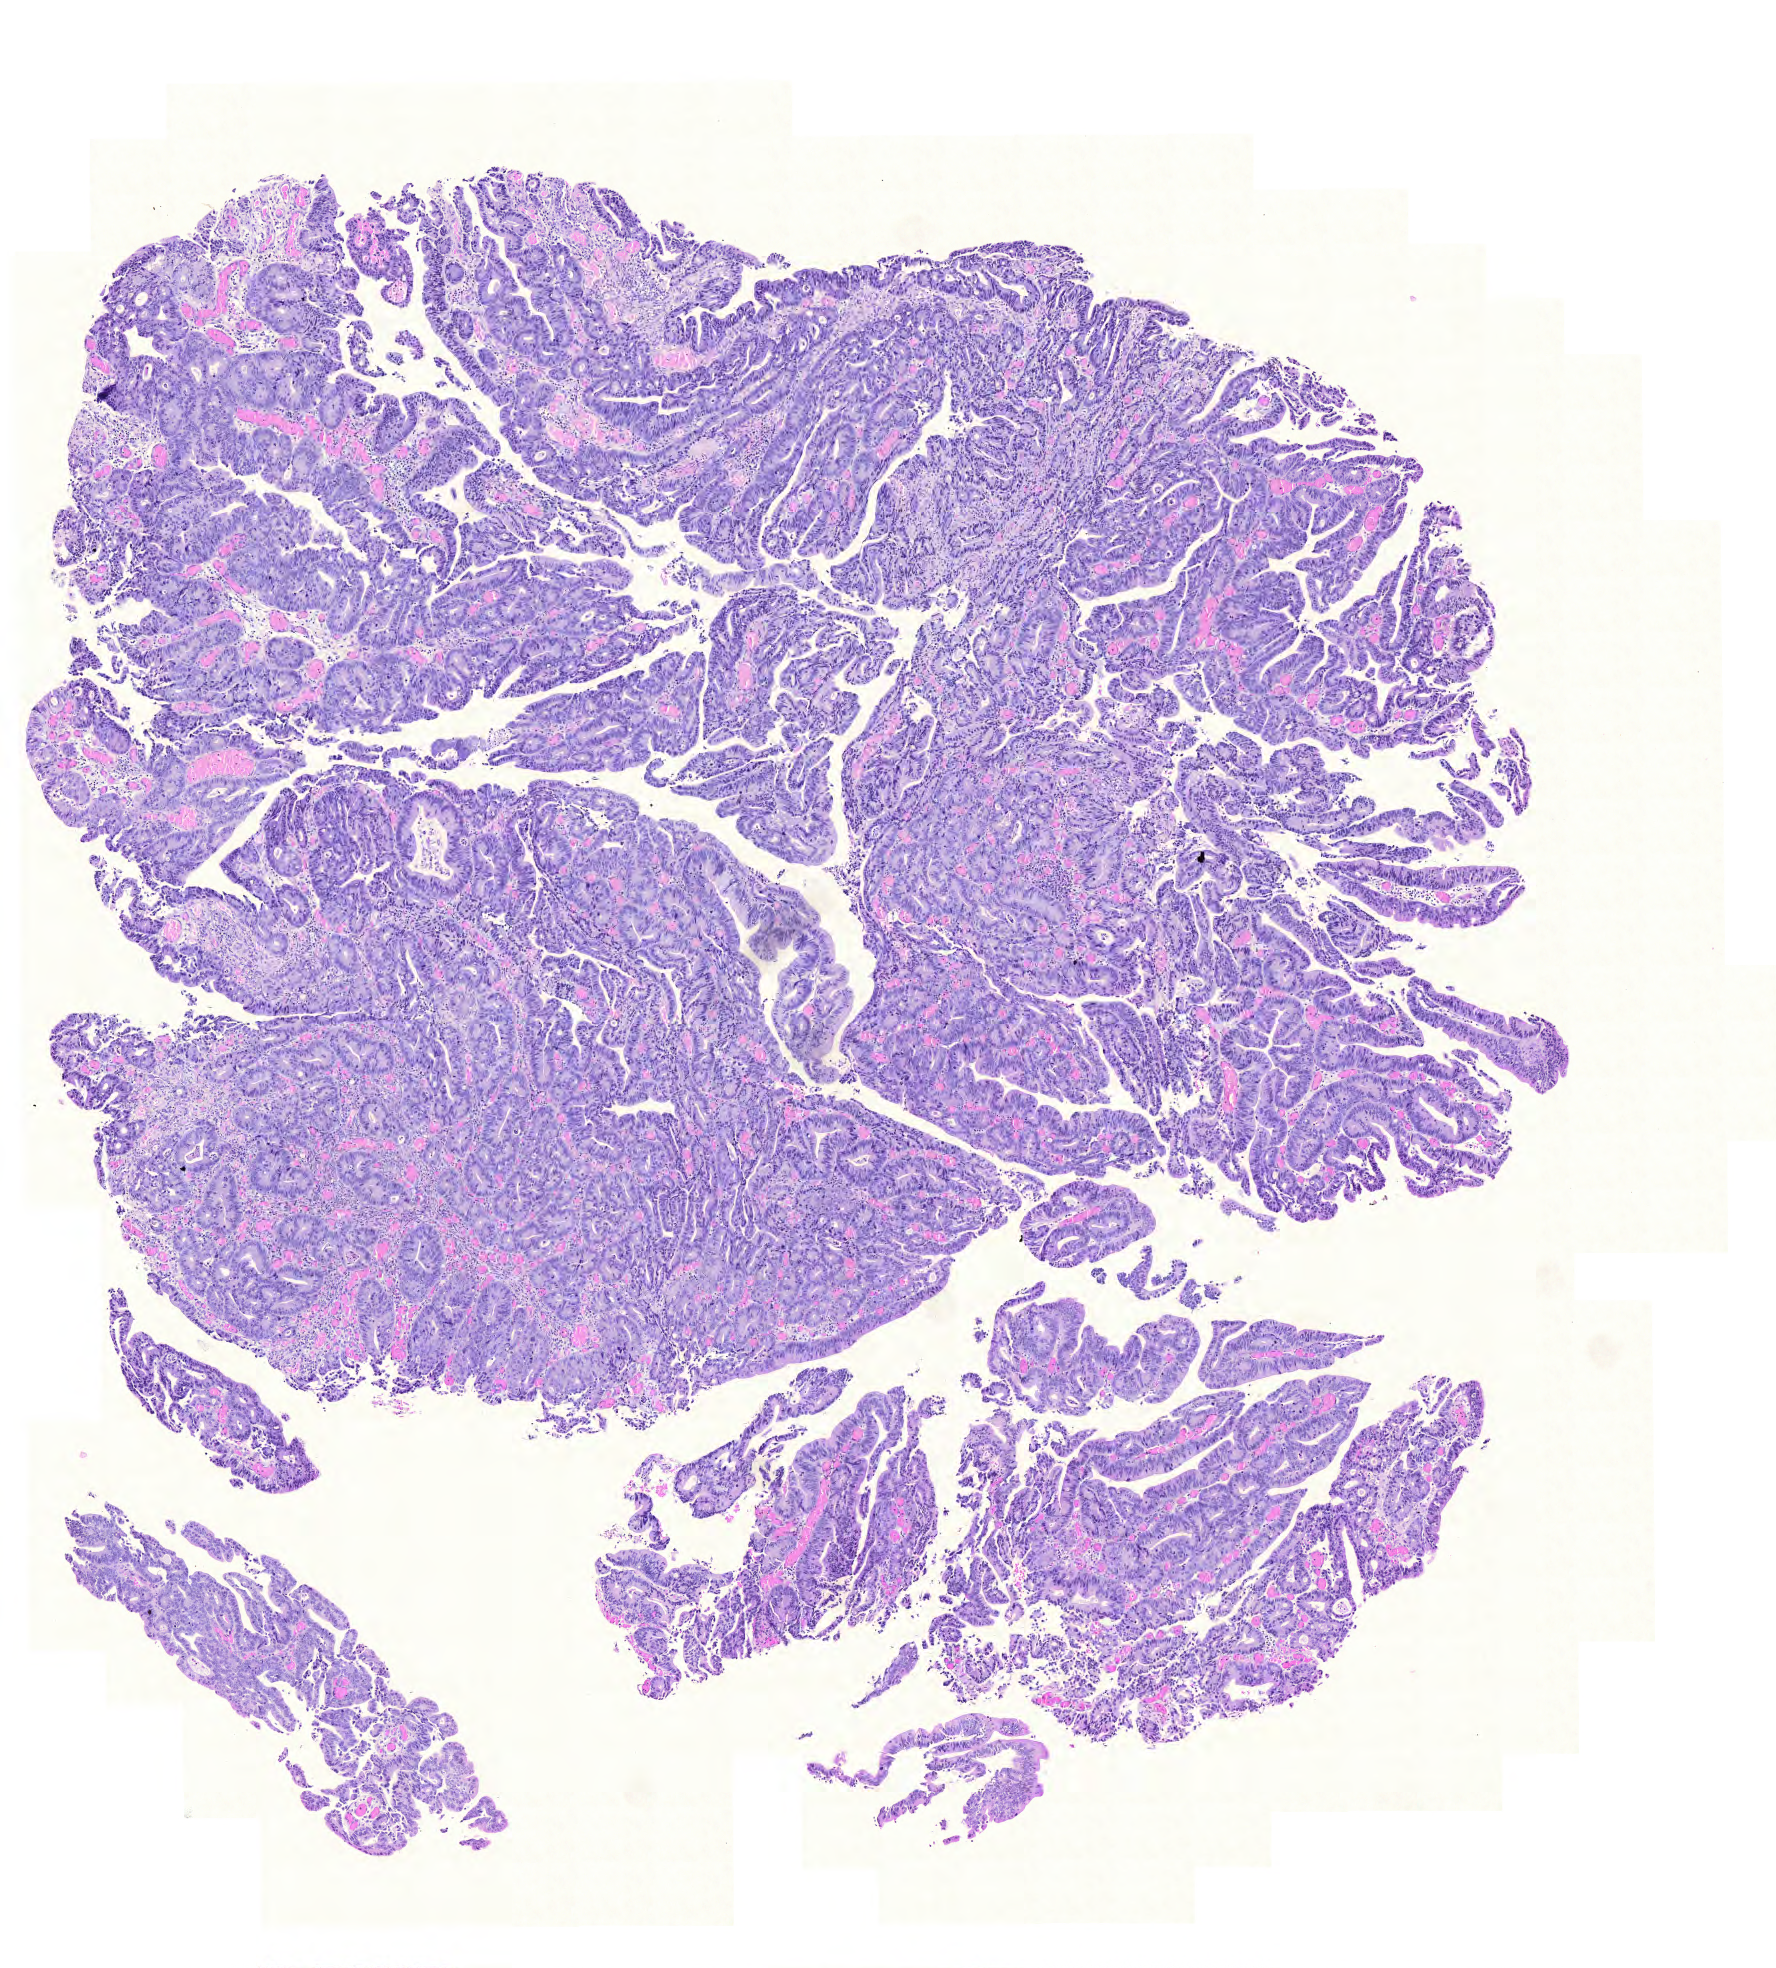
H&E whole-slide image, a low-resolution overview of the entire scanned area, about 6.6 x 7.3 mm, formalin-fixed paraffin-embedded (FFPE) diagnostic section, primary tumour sample from the rectum. Female, age 71 years at initial diagnosis.
AJCC pathologic stage: IIIB (6th edition). Histologic diagnosis: Adenocarcinoma, NOS.